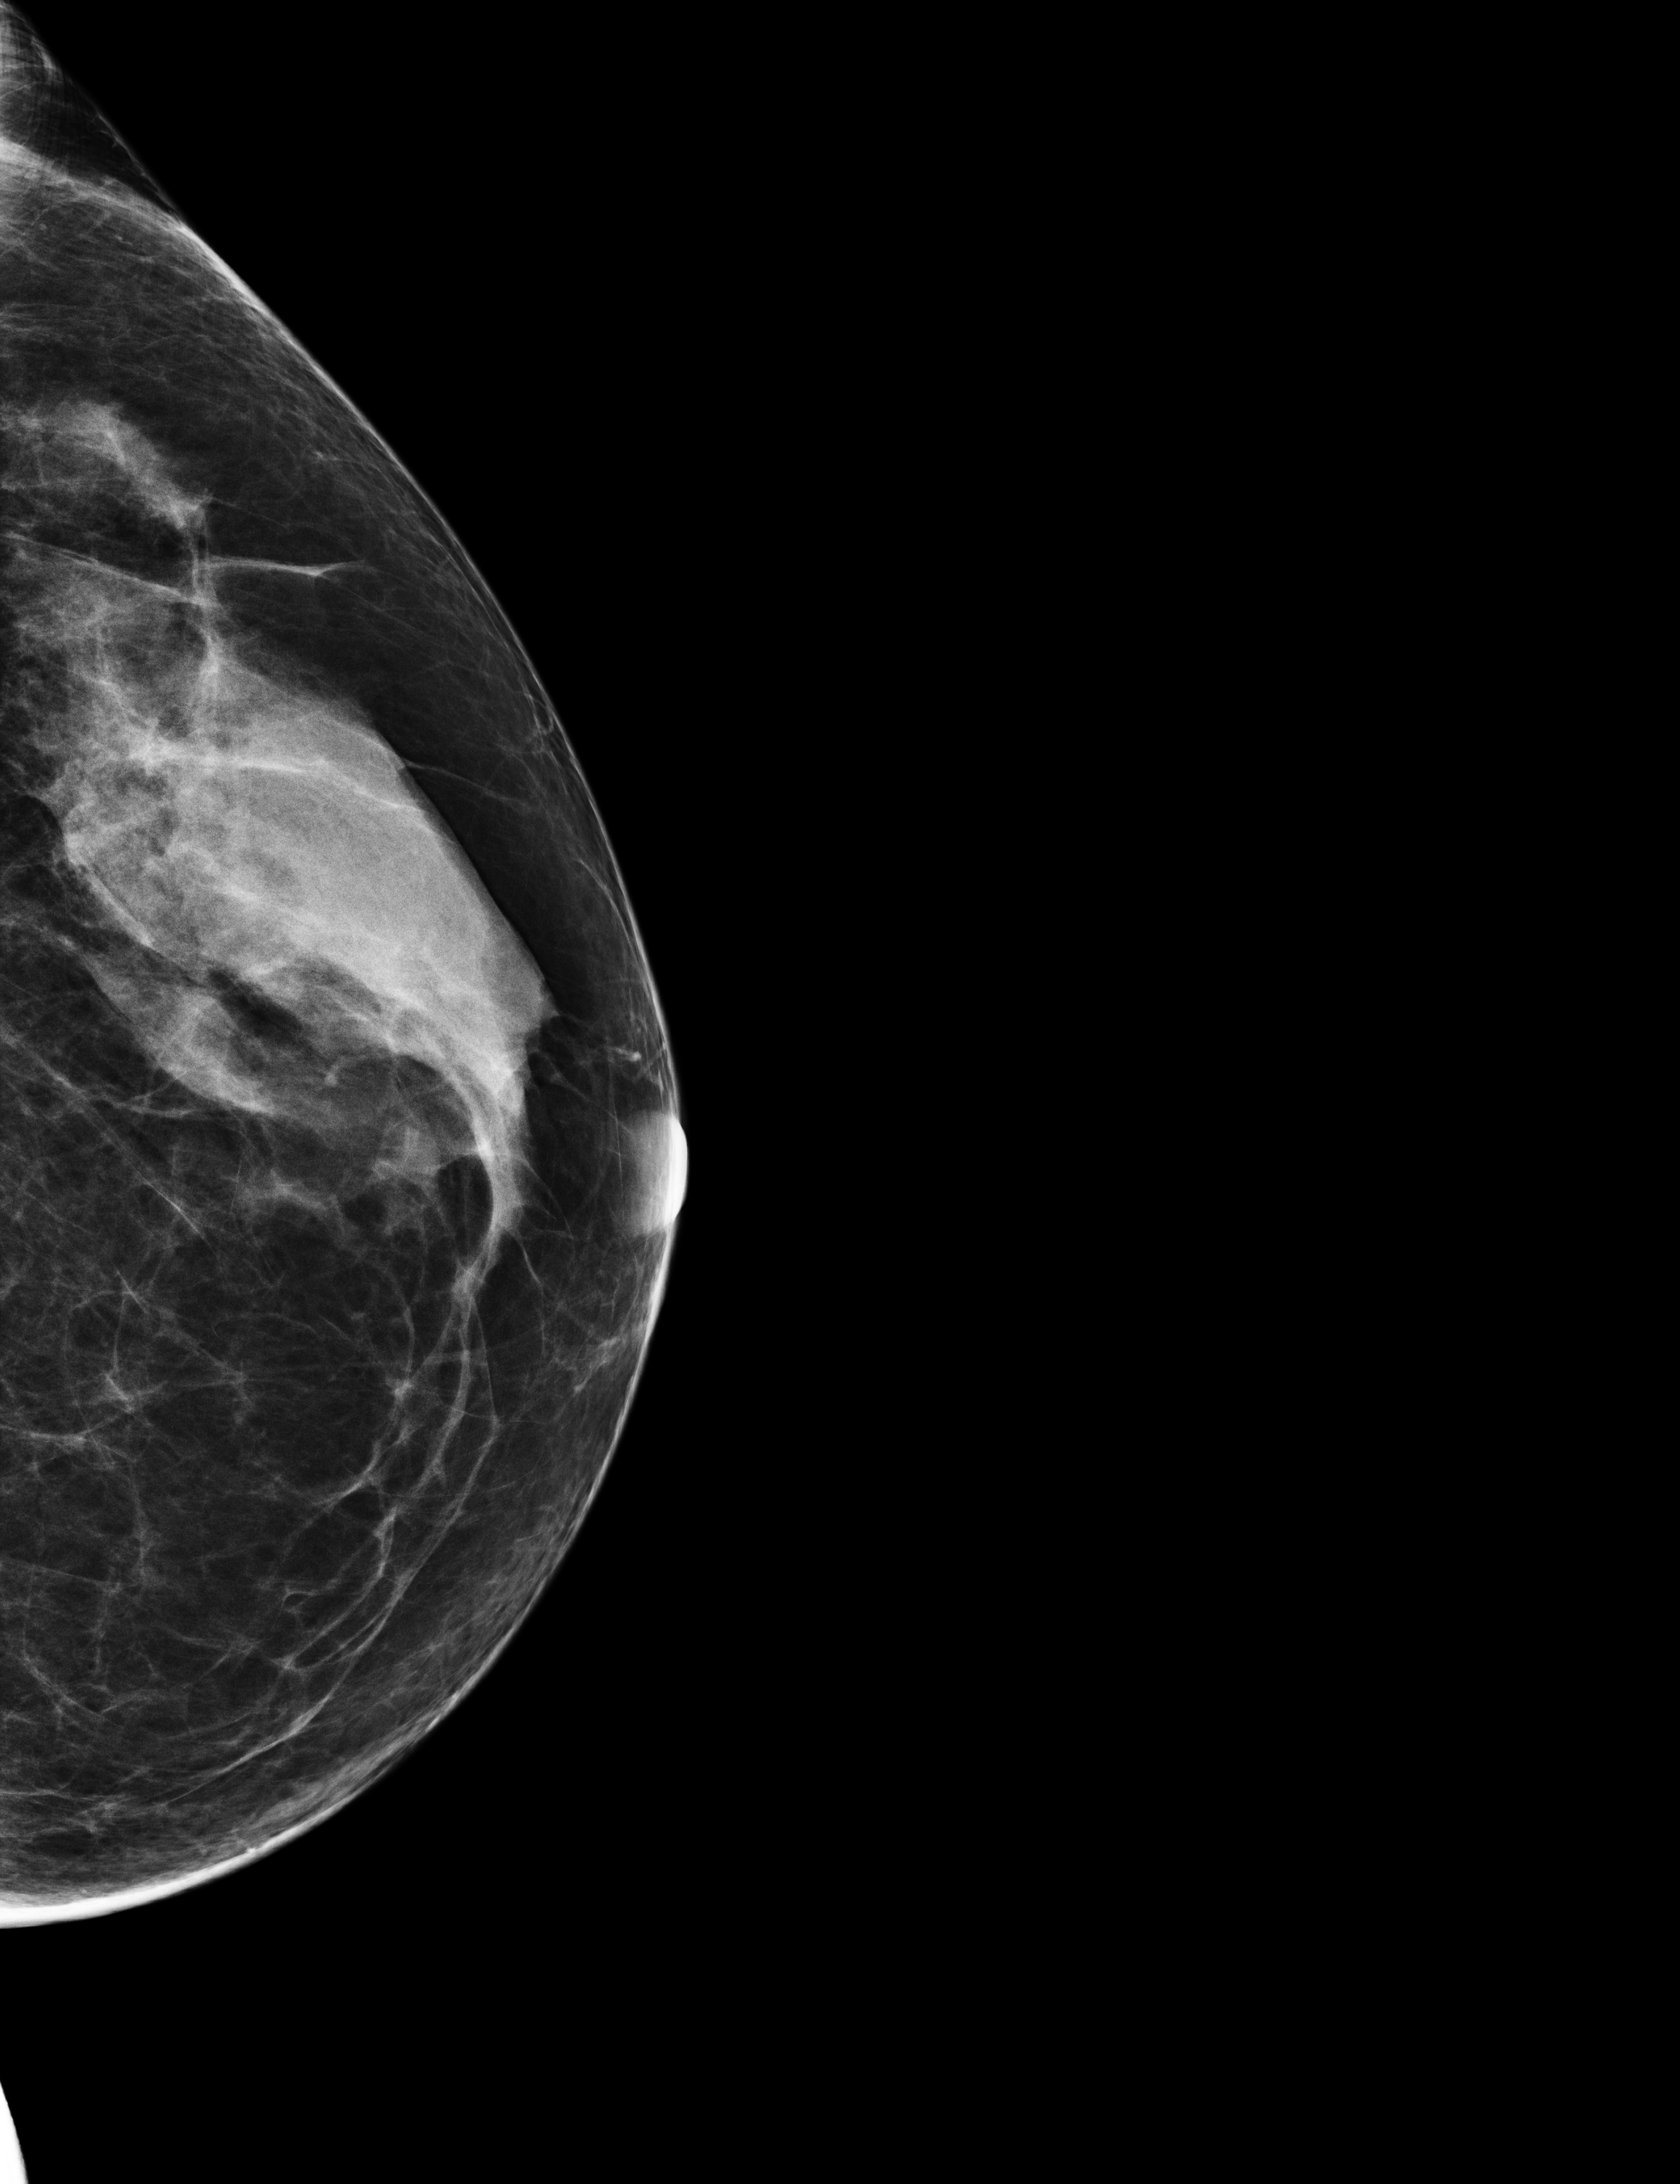
Digital mammogram (FFDM); left breast; CC view; screening examination; compressed breast thickness 57 mm; system: Selenia Dimensions. Female patient, age 66 years.
Breast density at the screening exam (both breasts): heterogeneously dense (BI-RADS density category c). Final BI-RADS assessment for this screening round (tomosynthesis exam, both breasts): category 1. Recall: no recall after this screen.